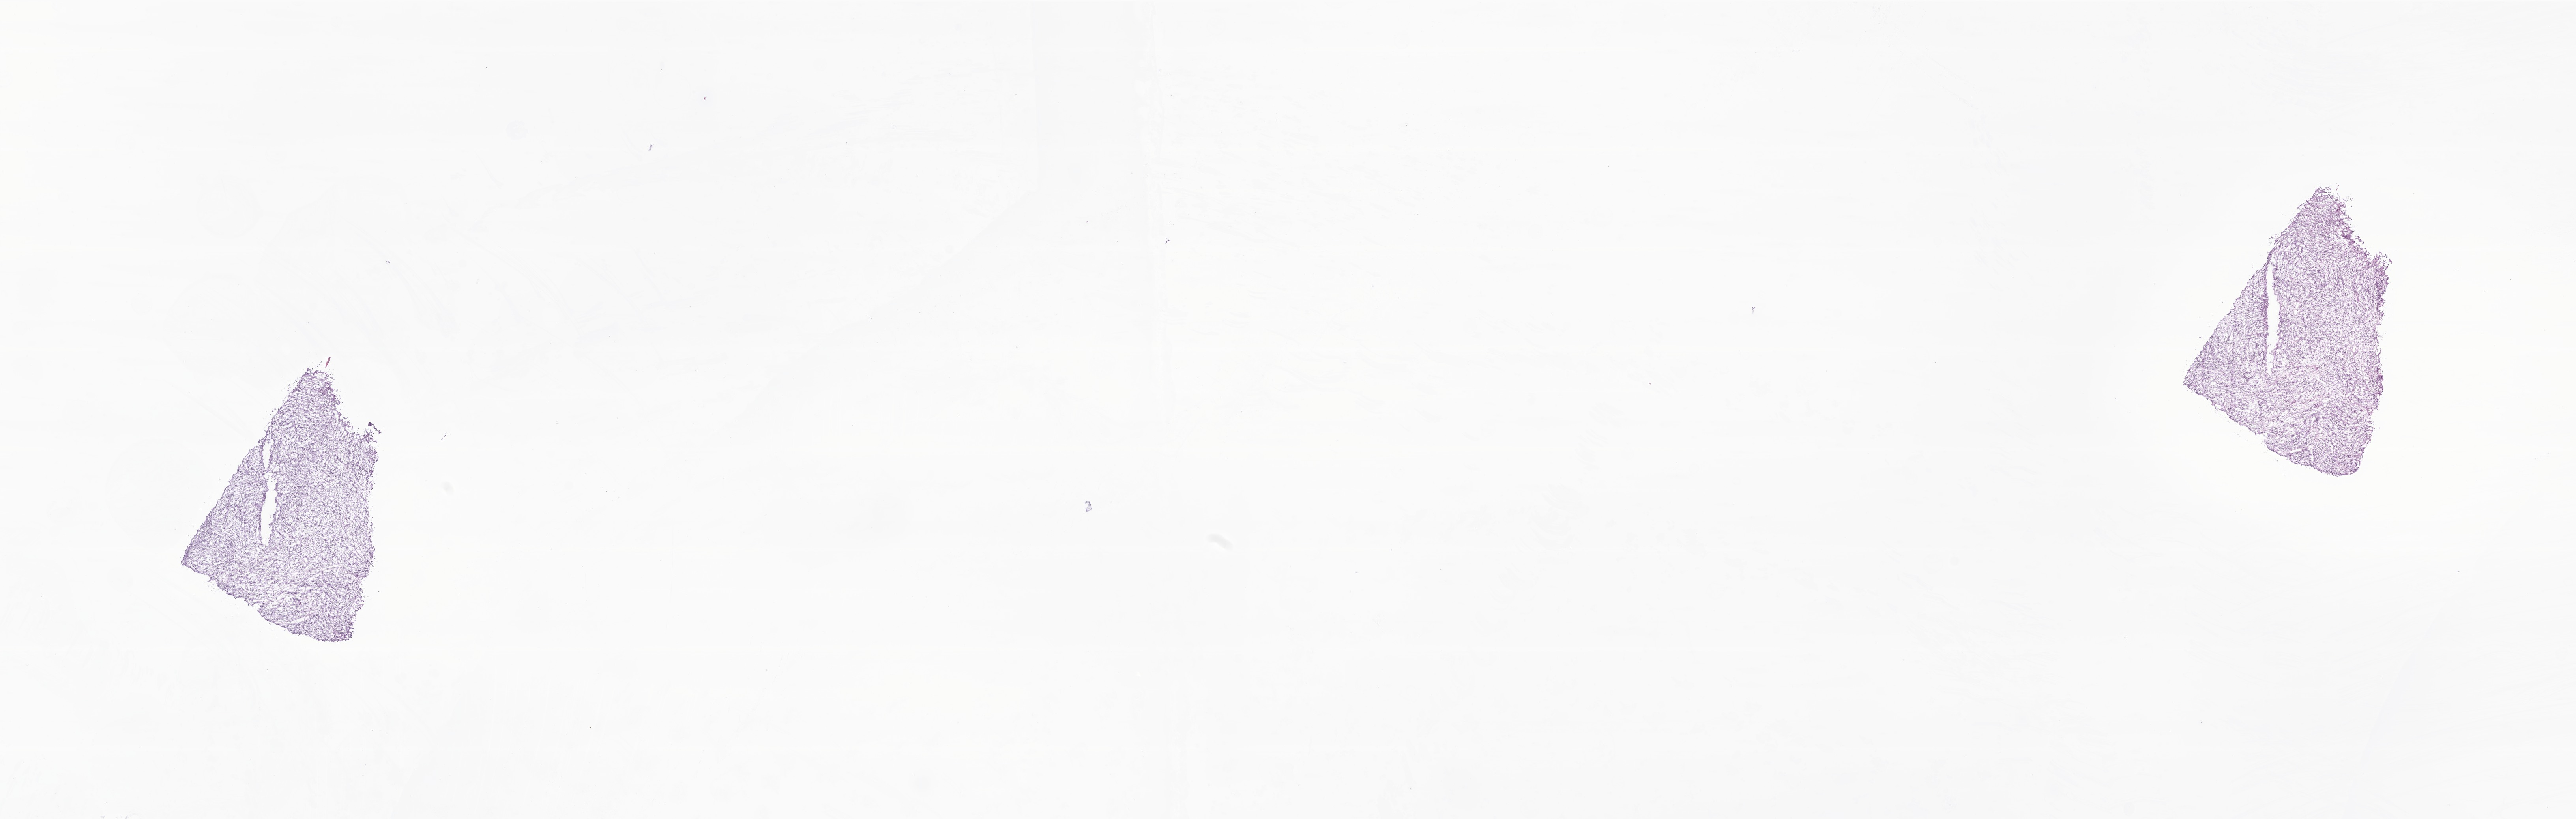
Hematoxylin and eosin (H&E) whole-slide image of tumor tissue from the abdomen, a low-resolution overview of the entire scanned area, about 27.5 x 8.8 mm, frozen section (OCT-embedded). Patient: female, age 92 months (7 years 8 months).
• diagnosis (ICD-O-3 morphology term): Rhabdomyosarcoma, NOS